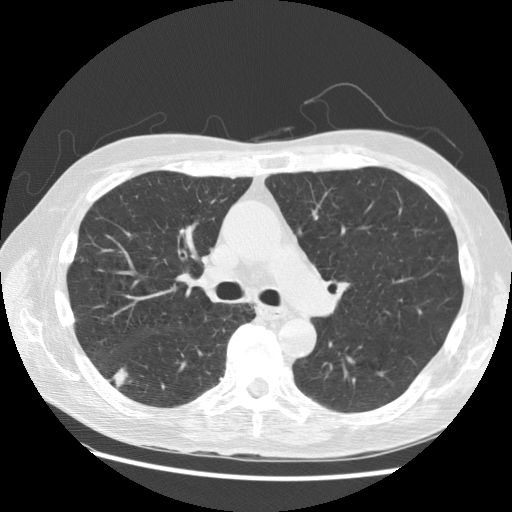
Low-dose screening chest CT, one axial slice; slice 101 of 168 in the series (ordered by position); reconstruction kernel STANDARD; 120 kVp; lung window (W 1500 / L -600 HU); 2.5 mm slice thickness; 512 × 512 image matrix.
Annotated regions visible in this slice (expert manual segmentation):
- lesion 1 (tumor, lower lobe of right lung): box from (x=114, y=369) to (x=127, y=387) px